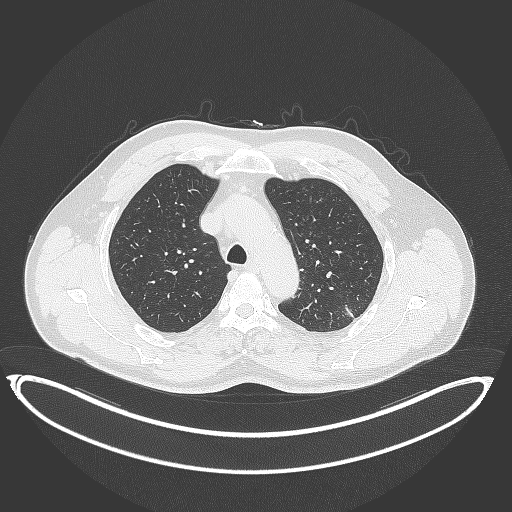
Chest CT, one axial slice. Slice 276 of 399 in the series (ordered by position). Reconstruction kernel B70f. 120 kVp. Lung window (W 1500 / L -600 HU). 1 mm slice thickness. 512 × 512 image matrix, field of view 469 × 469 mm. Male patient, age 58 years. Case-level facts recorded for this patient, not image findings: clinical TNM (as recorded): T1c N0 M0; histopathological grade: G1-2.
Structures marked on this image (bounding box drawn by a radiologist):
- lung tumour (recorded histology: adenocarcinoma): box from (x=340, y=300) to (x=360, y=325) px